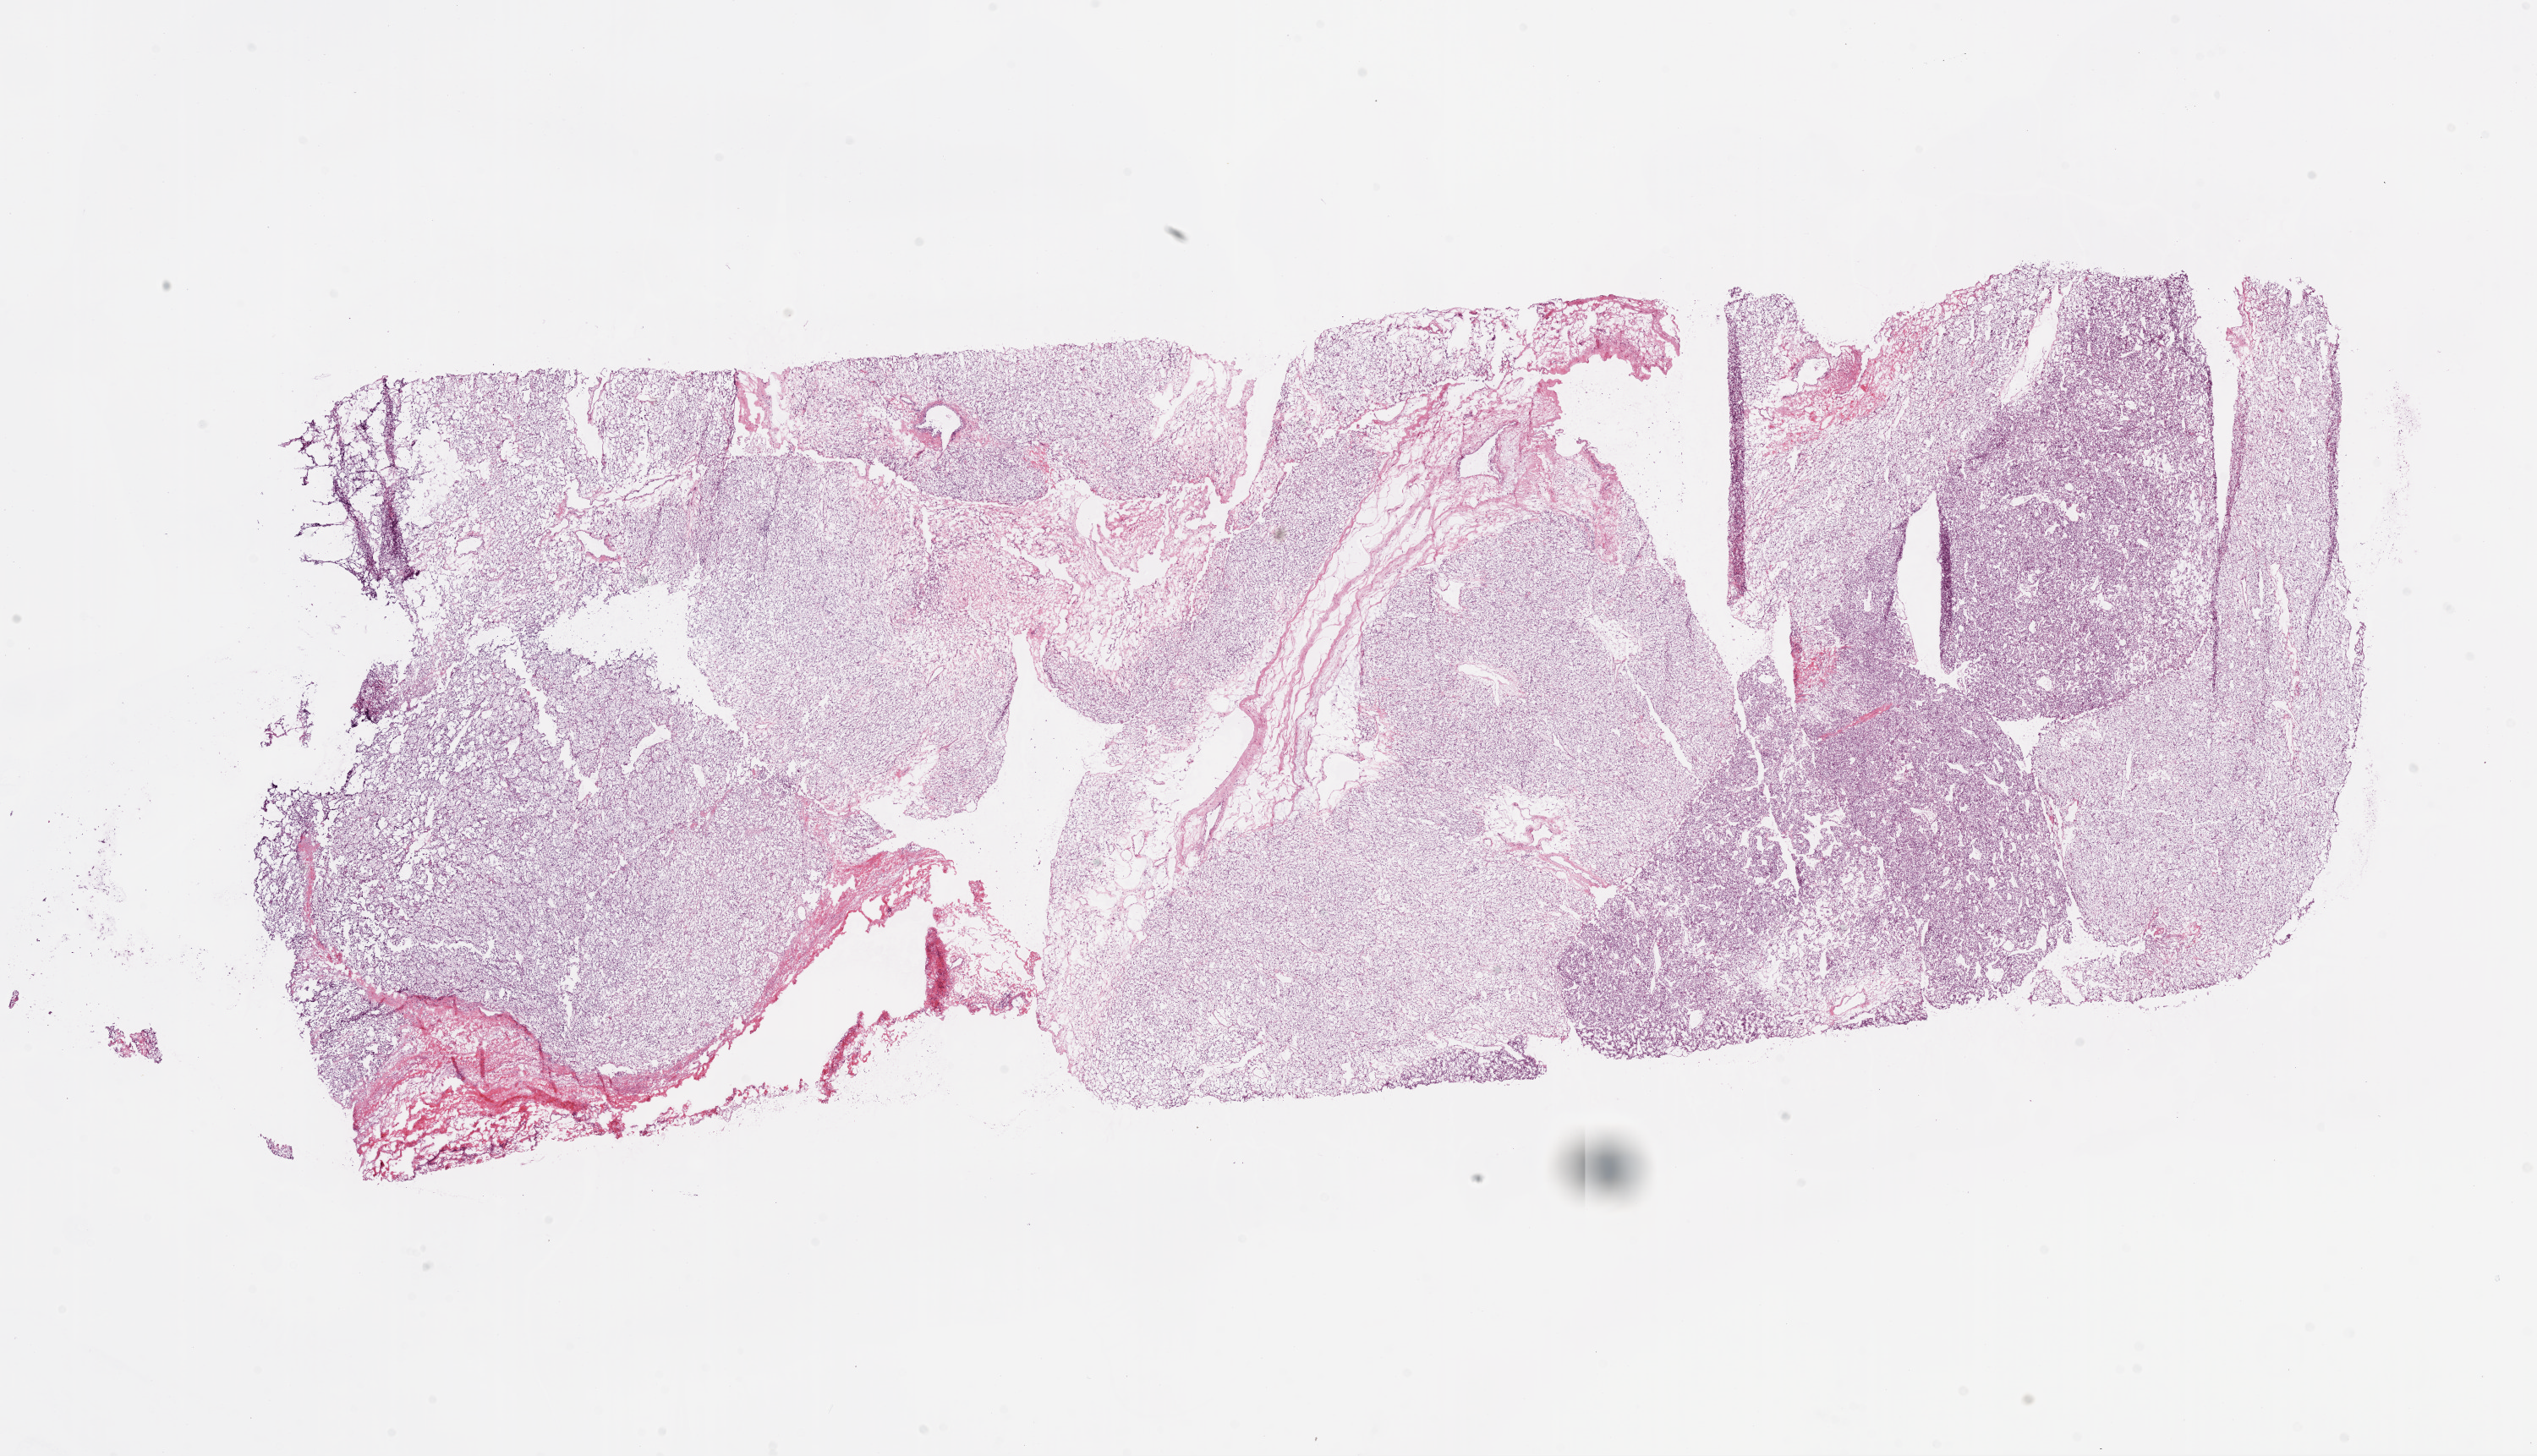
H&E whole-slide image — low-resolution overview of the scanned area, about 24.1 x 13.8 mm. Frozen section. Primary tumour sample from the kidney. Female patient; age at initial diagnosis 60 years. Histologic grade: G3 (poorly differentiated). Slide review estimates, as recorded: tumour cells 90%, tumour nuclei 85%, normal cells 0%, stromal cells 10%, necrosis 0%.
TNM: T3a N0 M1. Lymph nodes positive (case pathology): 0 of 13 examined. AJCC pathologic stage: IV. Diagnosis: Clear cell adenocarcinoma, NOS.